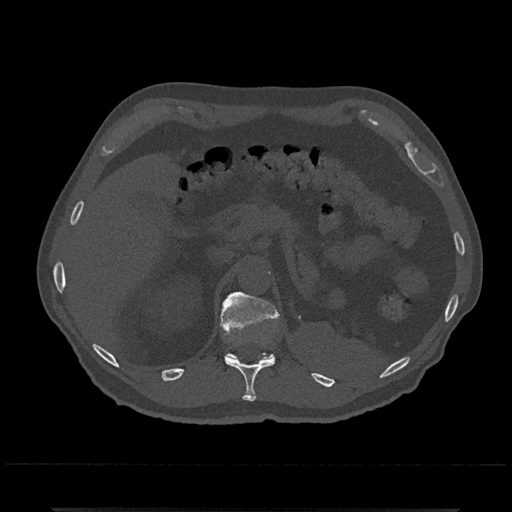
CT including the spine, one axial slice. Slice 466 of 797 in the series (ordered by position). Reconstruction kernel Br40s/3. 120 kVp. Bone window (W 1800 / L 400 HU). 0.5 mm slice thickness. 512 × 512 image matrix. Patient: male, 67 years. From the clinical record (not read from this slice): primary cancer: prostate.
Annotated regions visible in this slice (semi-automatically segmented with operator editing):
- T11 vertebra: bounding box [x1, y1, x2, y2] px = [225, 336, 276, 401]
- T12 vertebra: [220, 291, 281, 360]